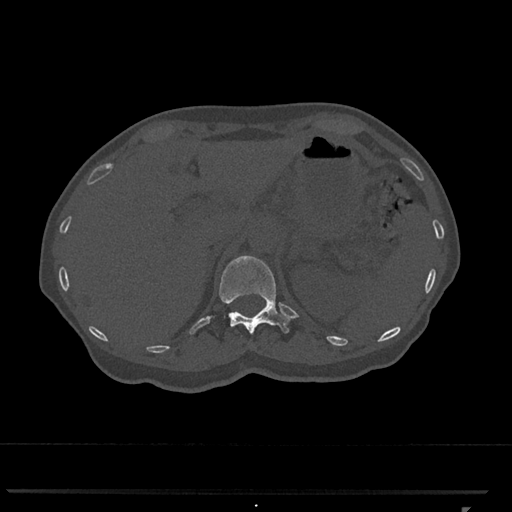
CT including the spine, one axial slice. Position 459 of 793 along the scan axis. Reconstruction kernel Br40s/3. Bone window (W 1800 / L 400 HU). 0.5 mm slice thickness. 512 × 512 image matrix. Patient: female, 62 years. Case-level facts recorded for this patient, not image findings: primary cancer: renal.
Outlined on this slice (semi-automatically segmented with operator editing):
- T12 vertebra: bounding box [x1, y1, x2, y2] px = [219, 255, 291, 335]